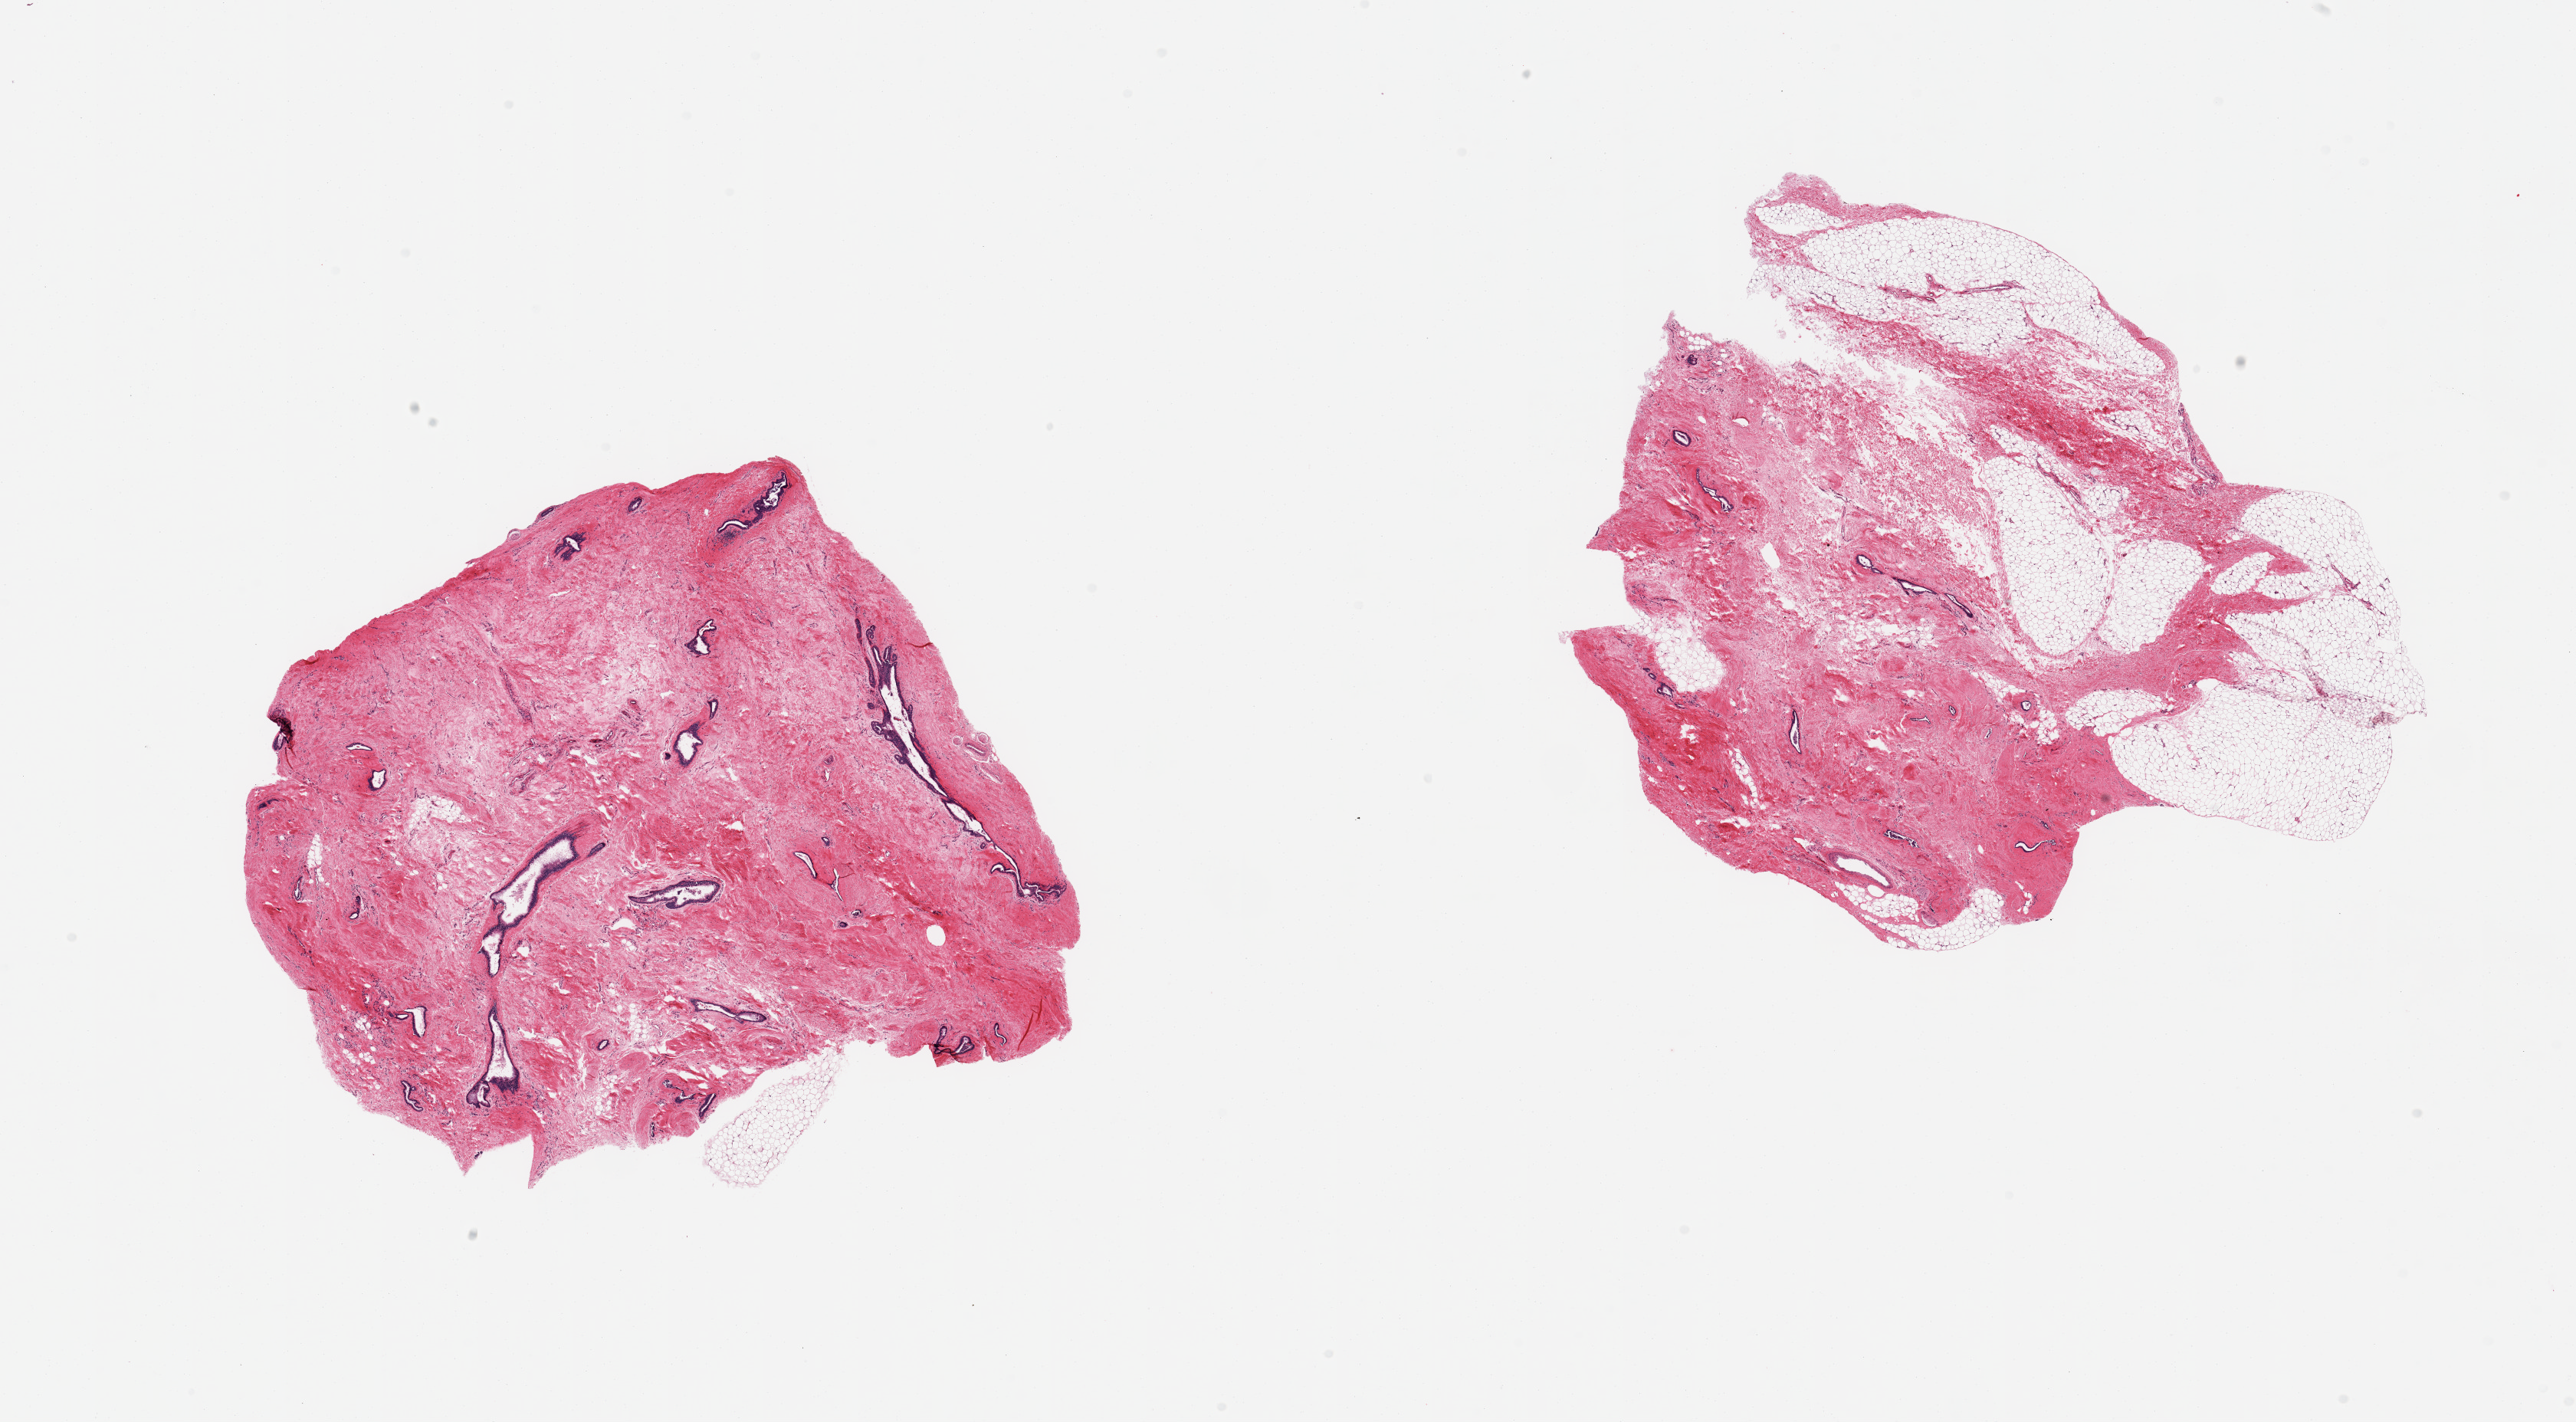
H&E whole-slide image, whole scanned area (about 26.6 x 14.7 mm, acquisition: 20x scan) shown as a low-resolution overview, PAXgene-fixed paraffin-embedded (PFPE) section, section of breast (target tissue), donor tissue sample. Male donor.
Review note (as recorded): 2 pieces, gynecomastoid stromal/duct hyerplasia; ductal elements.